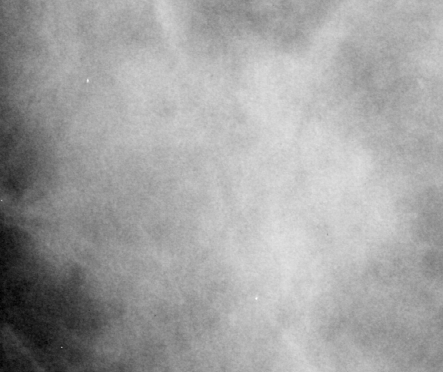
Cropped region of a digitized screen-film mammogram centred on a radiologist-marked abnormality, right breast, MLO view, BI-RADS breast density category 3 (scale 1–4).
Finding: mass, shape irregular, margins obscured / ill defined; BI-RADS assessment category 3; pathology (as recorded): malignant.